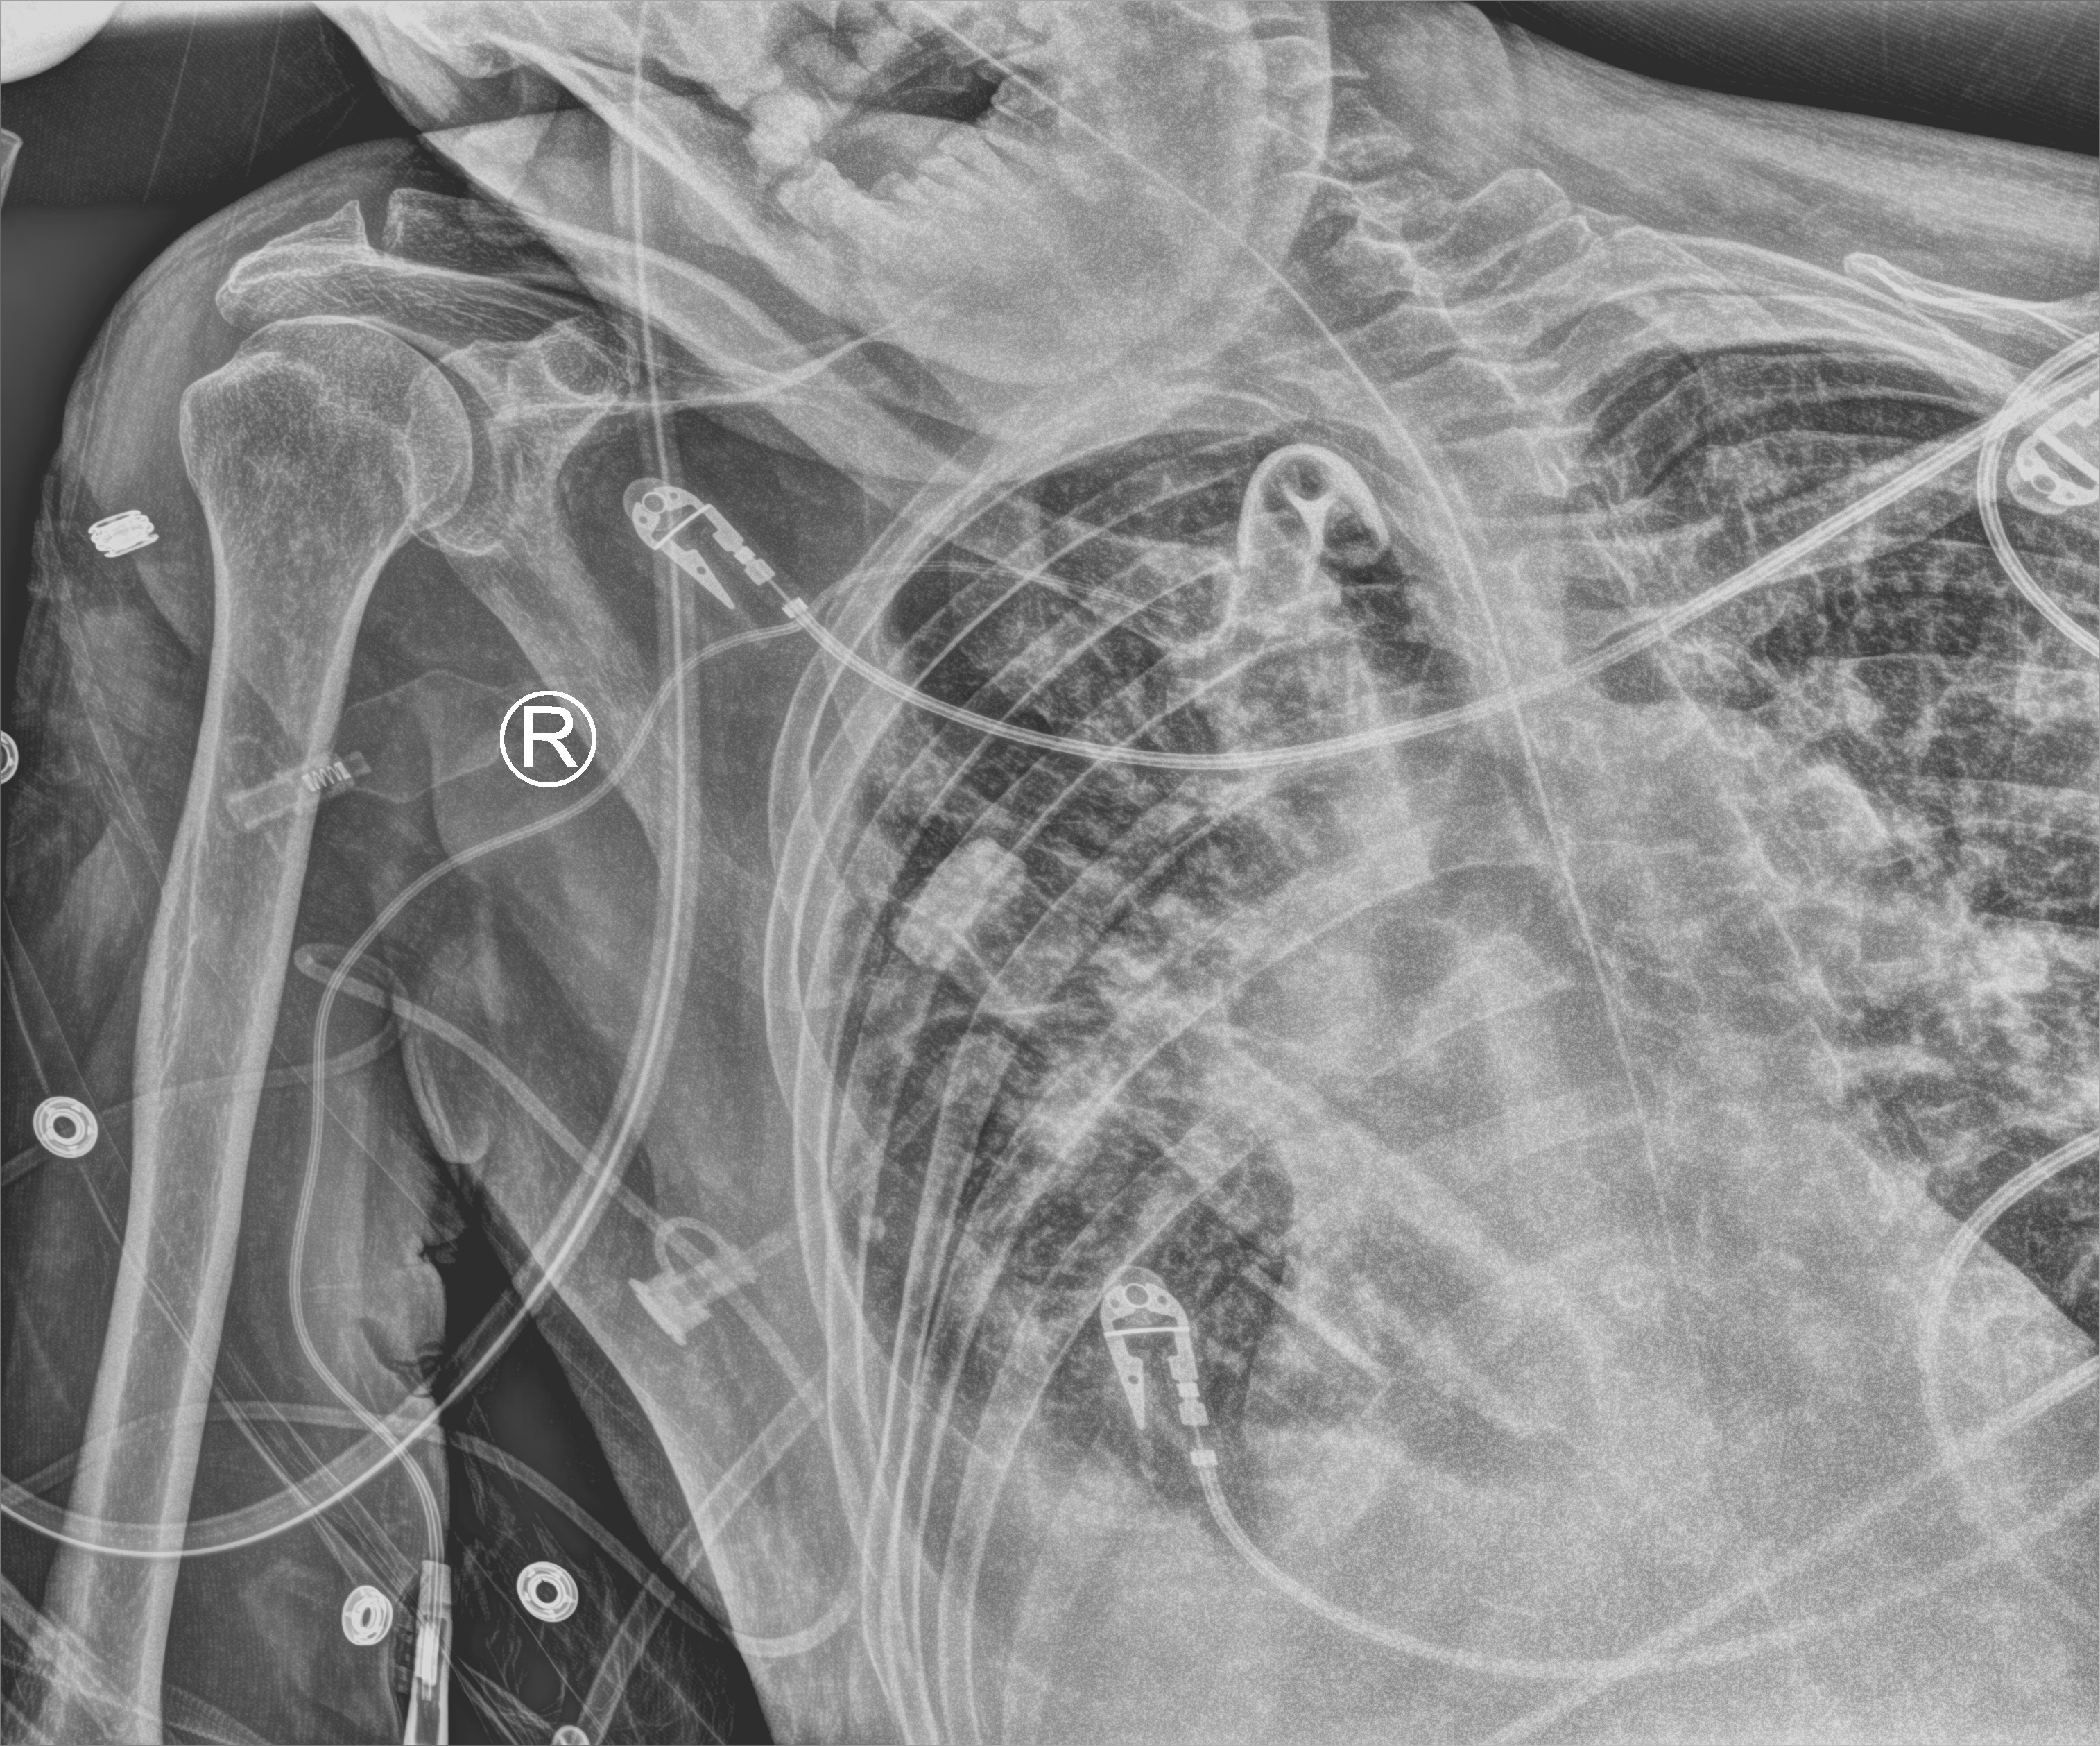
Bedside chest radiograph (computed radiography); anteroposterior (AP) projection. Male patient hospitalised with COVID-19, age 75–90 years.
Admission-level facts for this patient (not findings on this image; timing relative to this image not recorded): other chronic lung disease (admission record): yes.